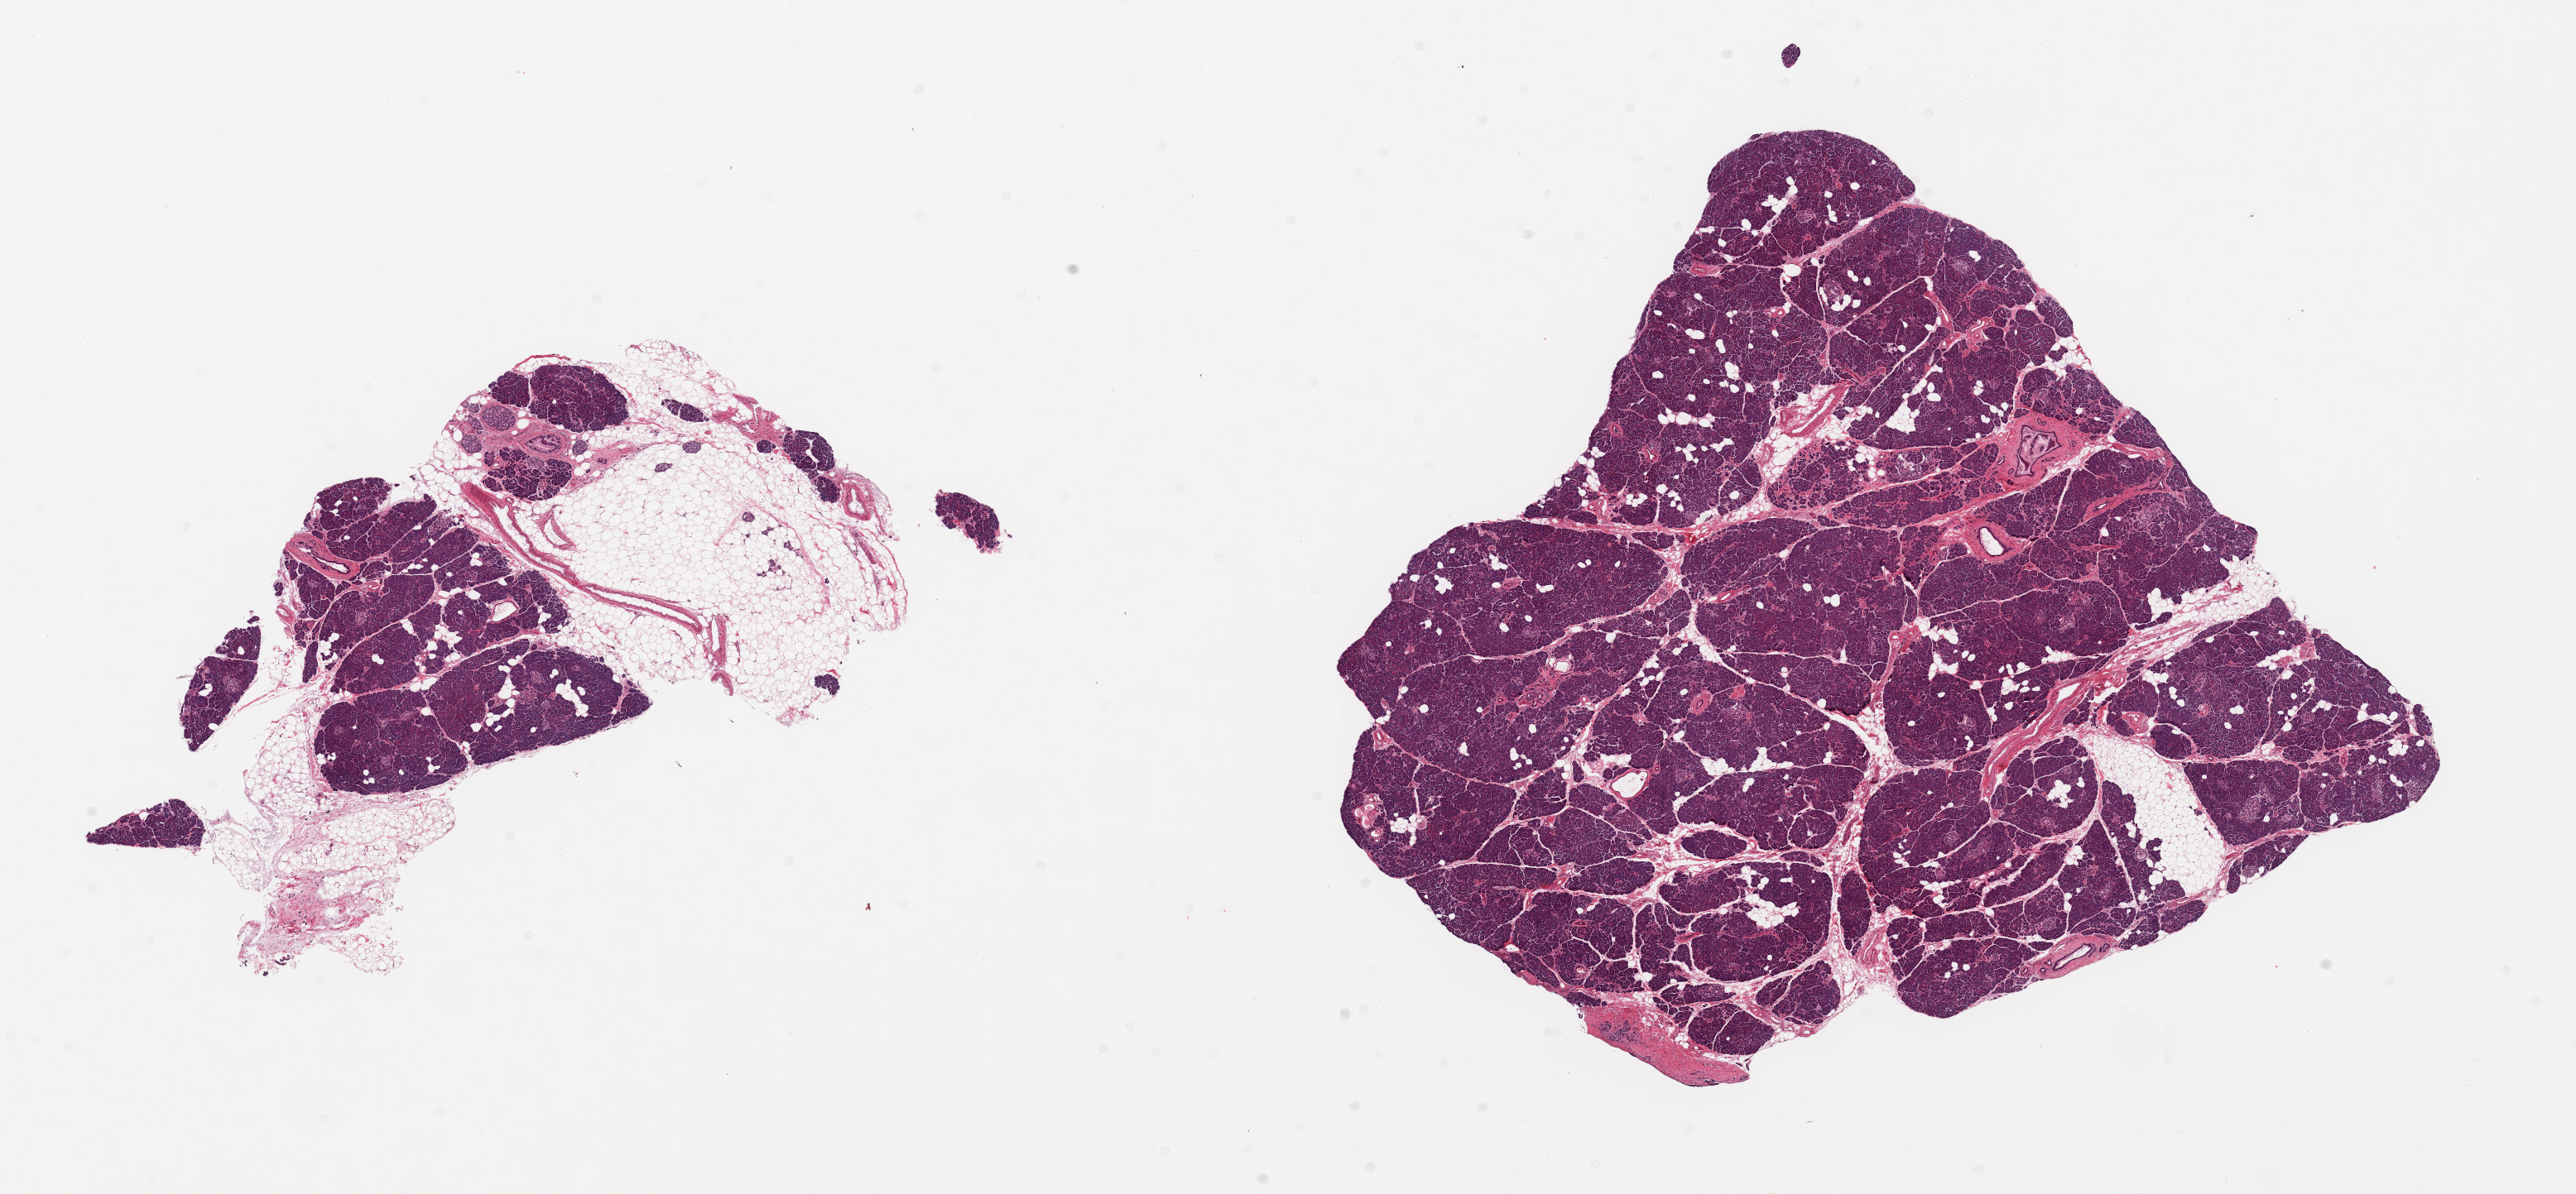
H&E whole-slide image, brightfield — shown as a low-resolution overview of the whole scanned area (about 24.6 x 11.4 mm, slide scanned at 20x), PAXgene-fixed paraffin-embedded (PFPE) section, sampled site (target tissue): pancreas, tissue donor sample. Donor: male.
Reviewer comment on this tissue sample: 2 pieces: 1 with 50% fat other with 5%; scattered focal exocrine atrophy and fibrosis; 2 ducts with PANin 1A changes.